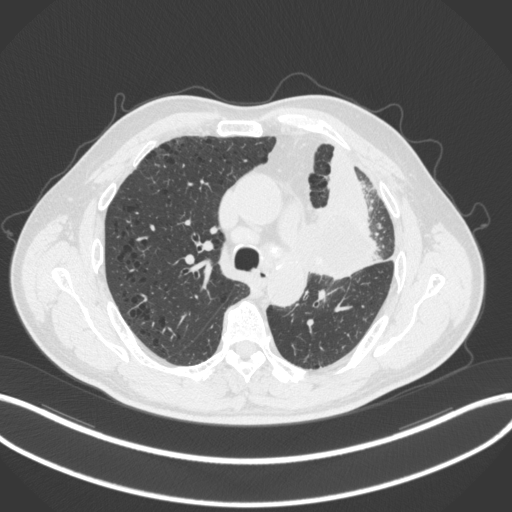
Chest CT, one axial slice; slice 194 of 286 in the series (ordered by position); reconstruction kernel B31f; lung window (W 1500 / L -600 HU); 1 mm slice thickness; 512 × 512 image matrix, field of view 400 × 400 mm. Male patient, age 68 years. Case-level facts recorded for this patient, not image findings: clinical TNM (as recorded): T3 N3 M1.
Structures marked on this image (bounding box drawn by a radiologist):
- lung tumour (recorded histology: adenocarcinoma): box from (x=292, y=194) to (x=378, y=281) px